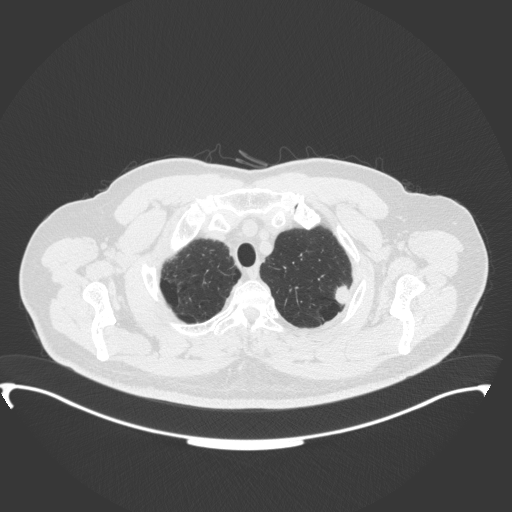
Chest CT, one axial slice; position 322 of 350 along the scan axis; reconstruction kernel B31f; lung window (W 1500 / L -600 HU); 512 × 512 image matrix. Male patient, age 64 years. Case-level facts recorded for this patient, not image findings: clinical TNM (as recorded): T1c N1 M1.
Structures marked on this image (rectangle marked by the reading radiologist):
- lung tumour (recorded histology: adenocarcinoma): bounding box <333,282,356,308> (left, top, right, bottom; pixels)